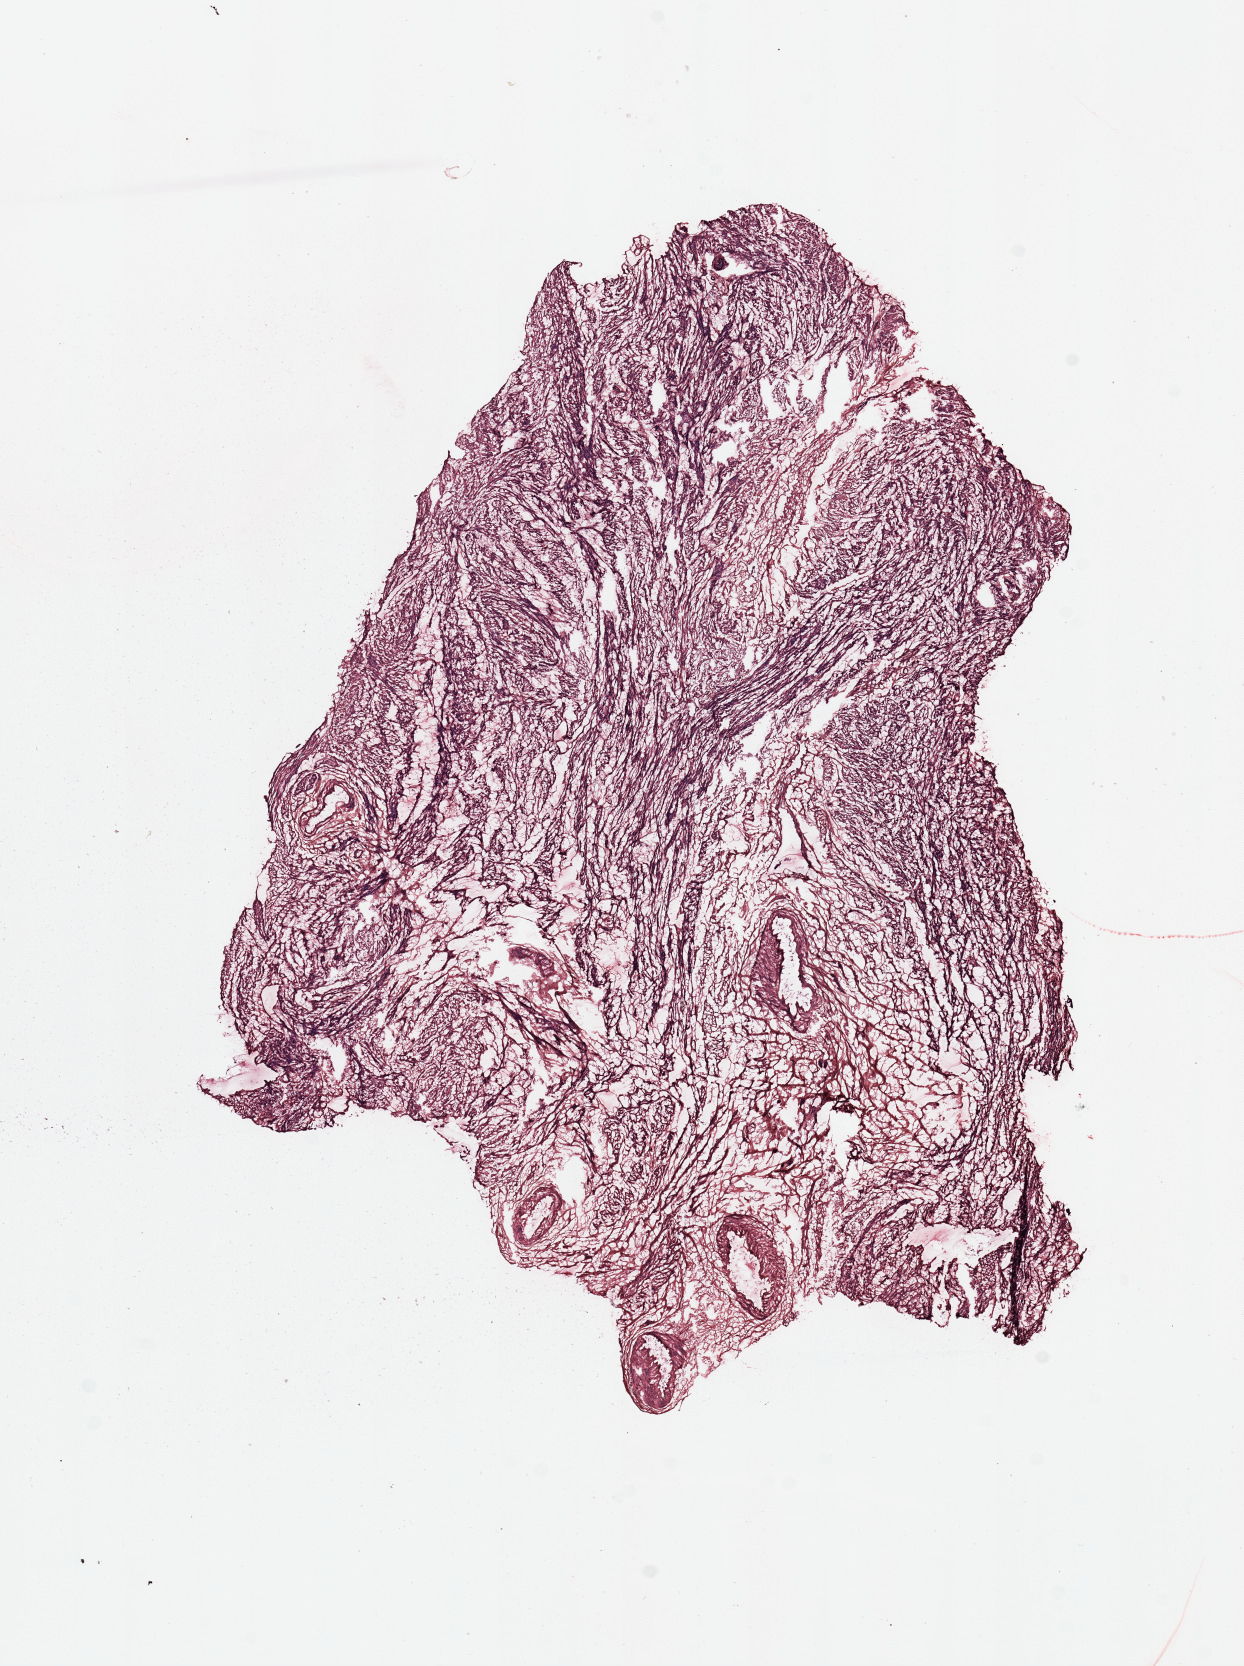
Digitized H&E tissue section (whole slide), whole scanned area (about 9.8 x 13.2 mm) shown as a low-resolution overview. Normal (non-tumour) tissue sample, uterus. Female, 68 y/o.
• this section: normal (non-tumour) tissue from the same patient
• patient diagnosis: Endometrioid adenocarcinoma, NOS